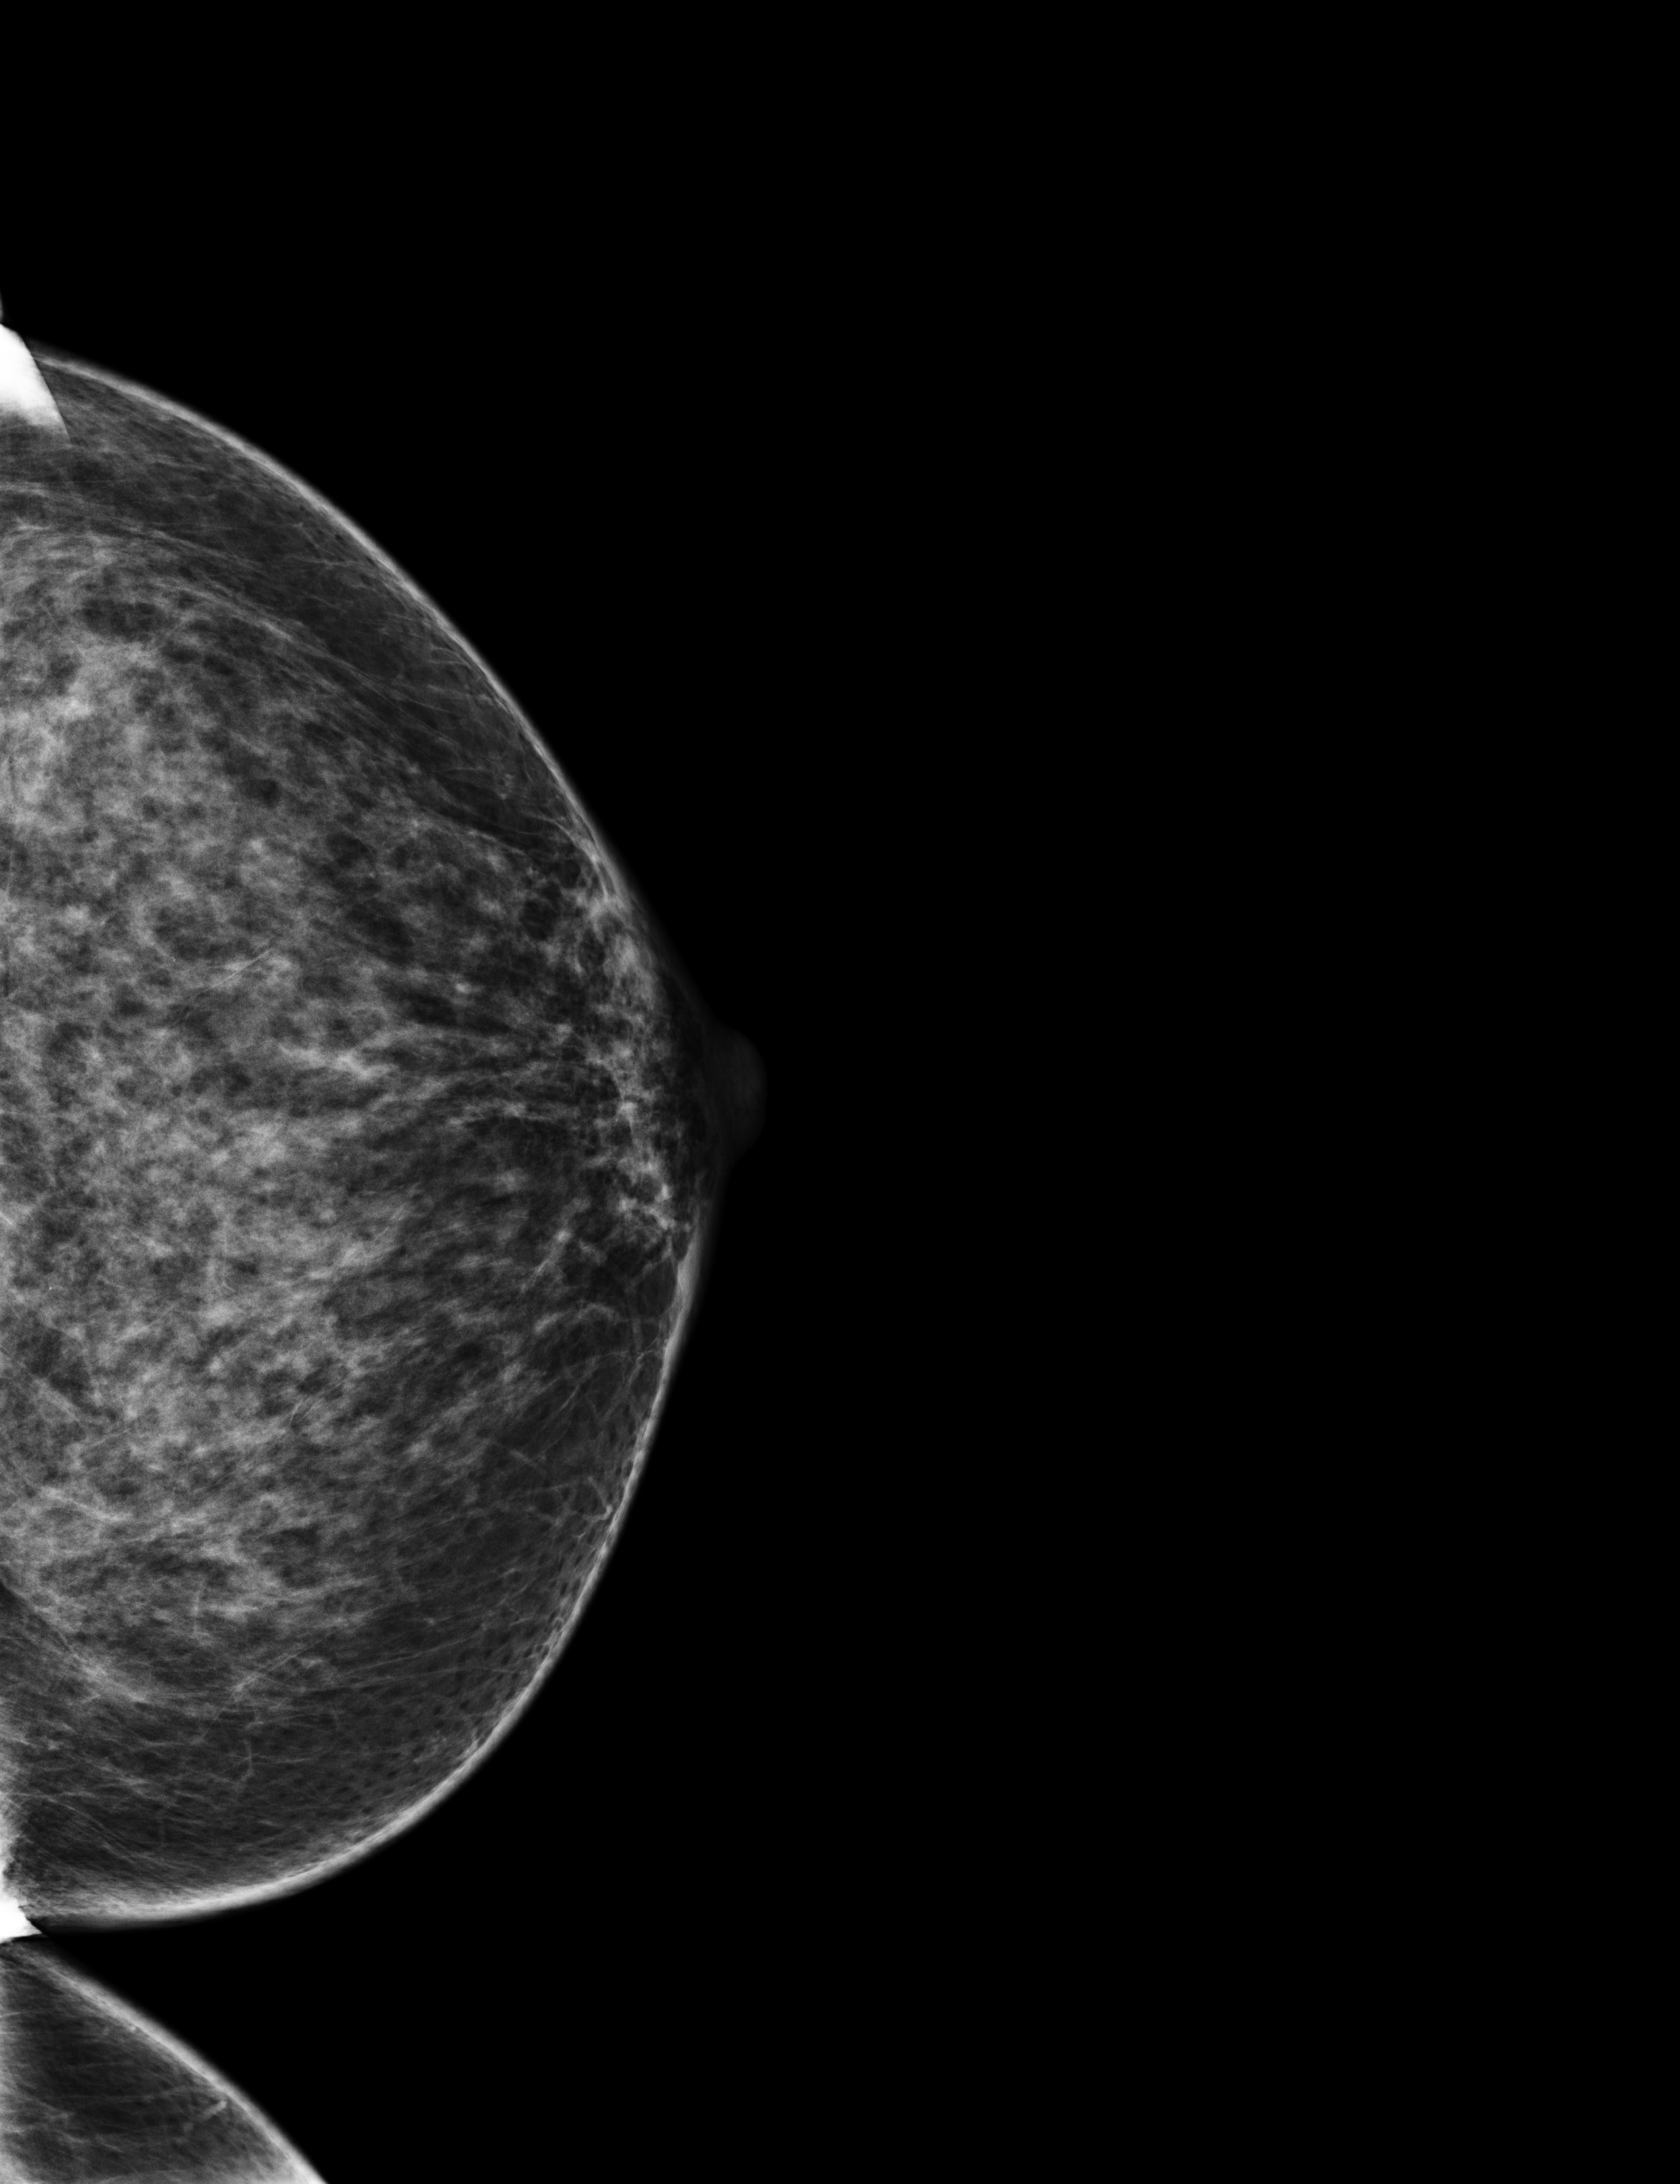
Annual screening mammography examination, system: Selenia Dimensions. Patient aged 53 years (female).
Image type: full-field digital mammogram. Breast: left. Projection: craniocaudal (CC) view.